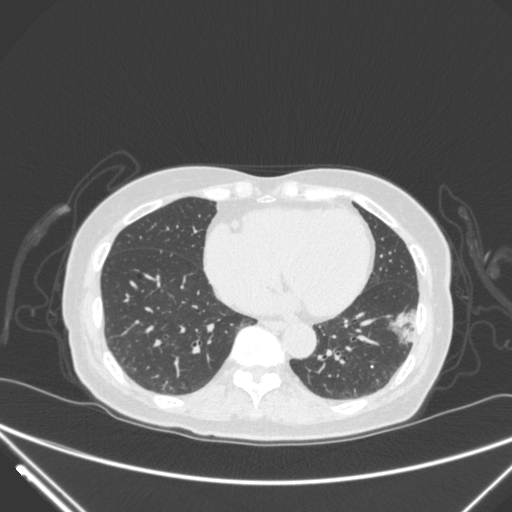
Chest CT, one axial slice. Lung window (W 1500 / L -600 HU). 1 mm slice thickness. 512 × 512 image matrix. Female patient, age 82 years. Case-level facts recorded for this patient, not image findings: clinical TNM (as recorded): T1c N0 M0; histopathological grade: G2.
Outlined on this slice (bounding box drawn by a radiologist):
- lung tumour (recorded histology: adenocarcinoma): bounding box [x1, y1, x2, y2] px = [381, 303, 434, 368]